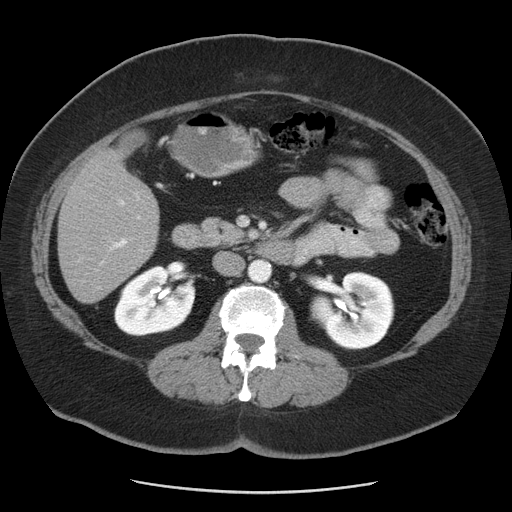
Contrast-enhanced abdominal CT, one axial slice; position 18 of 55 along the scan axis; 120 kVp; intravenous contrast given; soft-tissue window (W 400 / L 40 HU); 5 mm slice thickness; 512 × 512 image matrix, field of view 380 × 380 mm. Female patient, age 52 years. Case-level facts recorded for this patient, not image findings: diagnosis: colorectal cancer liver metastases, imaged before liver resection; multiple liver metastases: yes; largest metastasis: 2.5 cm.
Annotated regions visible in this slice (expert manual segmentation):
- liver: bounding box [x1, y1, x2, y2] px = [59, 131, 160, 303]
- planned liver remnant (the part of the liver to remain after resection): [58, 189, 152, 303]
- portal vein (with intrahepatic branches): [108, 192, 143, 252]
- liver metastasis: [120, 130, 146, 153]